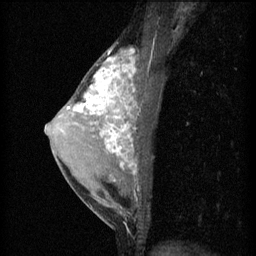
Breast MRI (dynamic contrast-enhanced), one sagittal slice; position 33 of 60 along the scan axis; 3 images stored at this slice position (order not interpretable as contrast timing); 1.5 T; TE 4.2 ms, TR 11 ms; 256 × 256 image matrix. Female patient, age 40 years.
Outlined on this slice (semi-automatic segmentation, software-assisted and operator-edited):
- analysis volume of interest (the breast-tissue region the enhancement analysis was run in; not a lesion): bounding box <55,46,151,203> (left, top, right, bottom; pixels)
- tumour enhancement mask (voxels above the 70 % enhancement threshold inside the analysis volume of interest): <68,50,138,197>